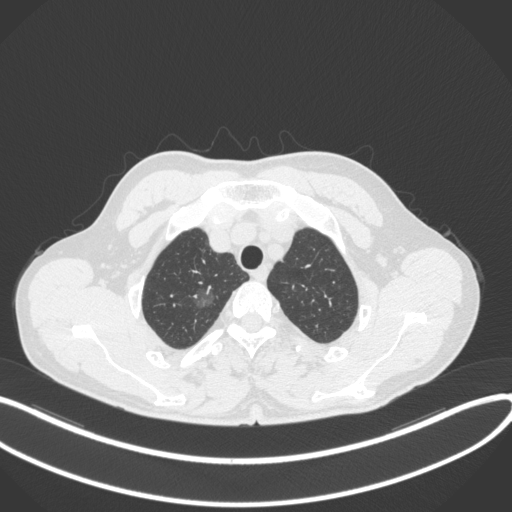
Chest CT, one axial slice. Position 325 of 407 along the scan axis. Reconstruction kernel B31f. 120 kVp. Lung window (W 1500 / L -600 HU). 1 mm slice thickness. 512 × 512 image matrix. Patient: male, 58 years. Case-level facts recorded for this patient, not image findings: clinical TNM (as recorded): T1c N0 M0.
Structures marked on this image (rectangle marked by the reading radiologist):
- lung tumour (recorded histology: adenocarcinoma): box from (x=187, y=276) to (x=221, y=307) px